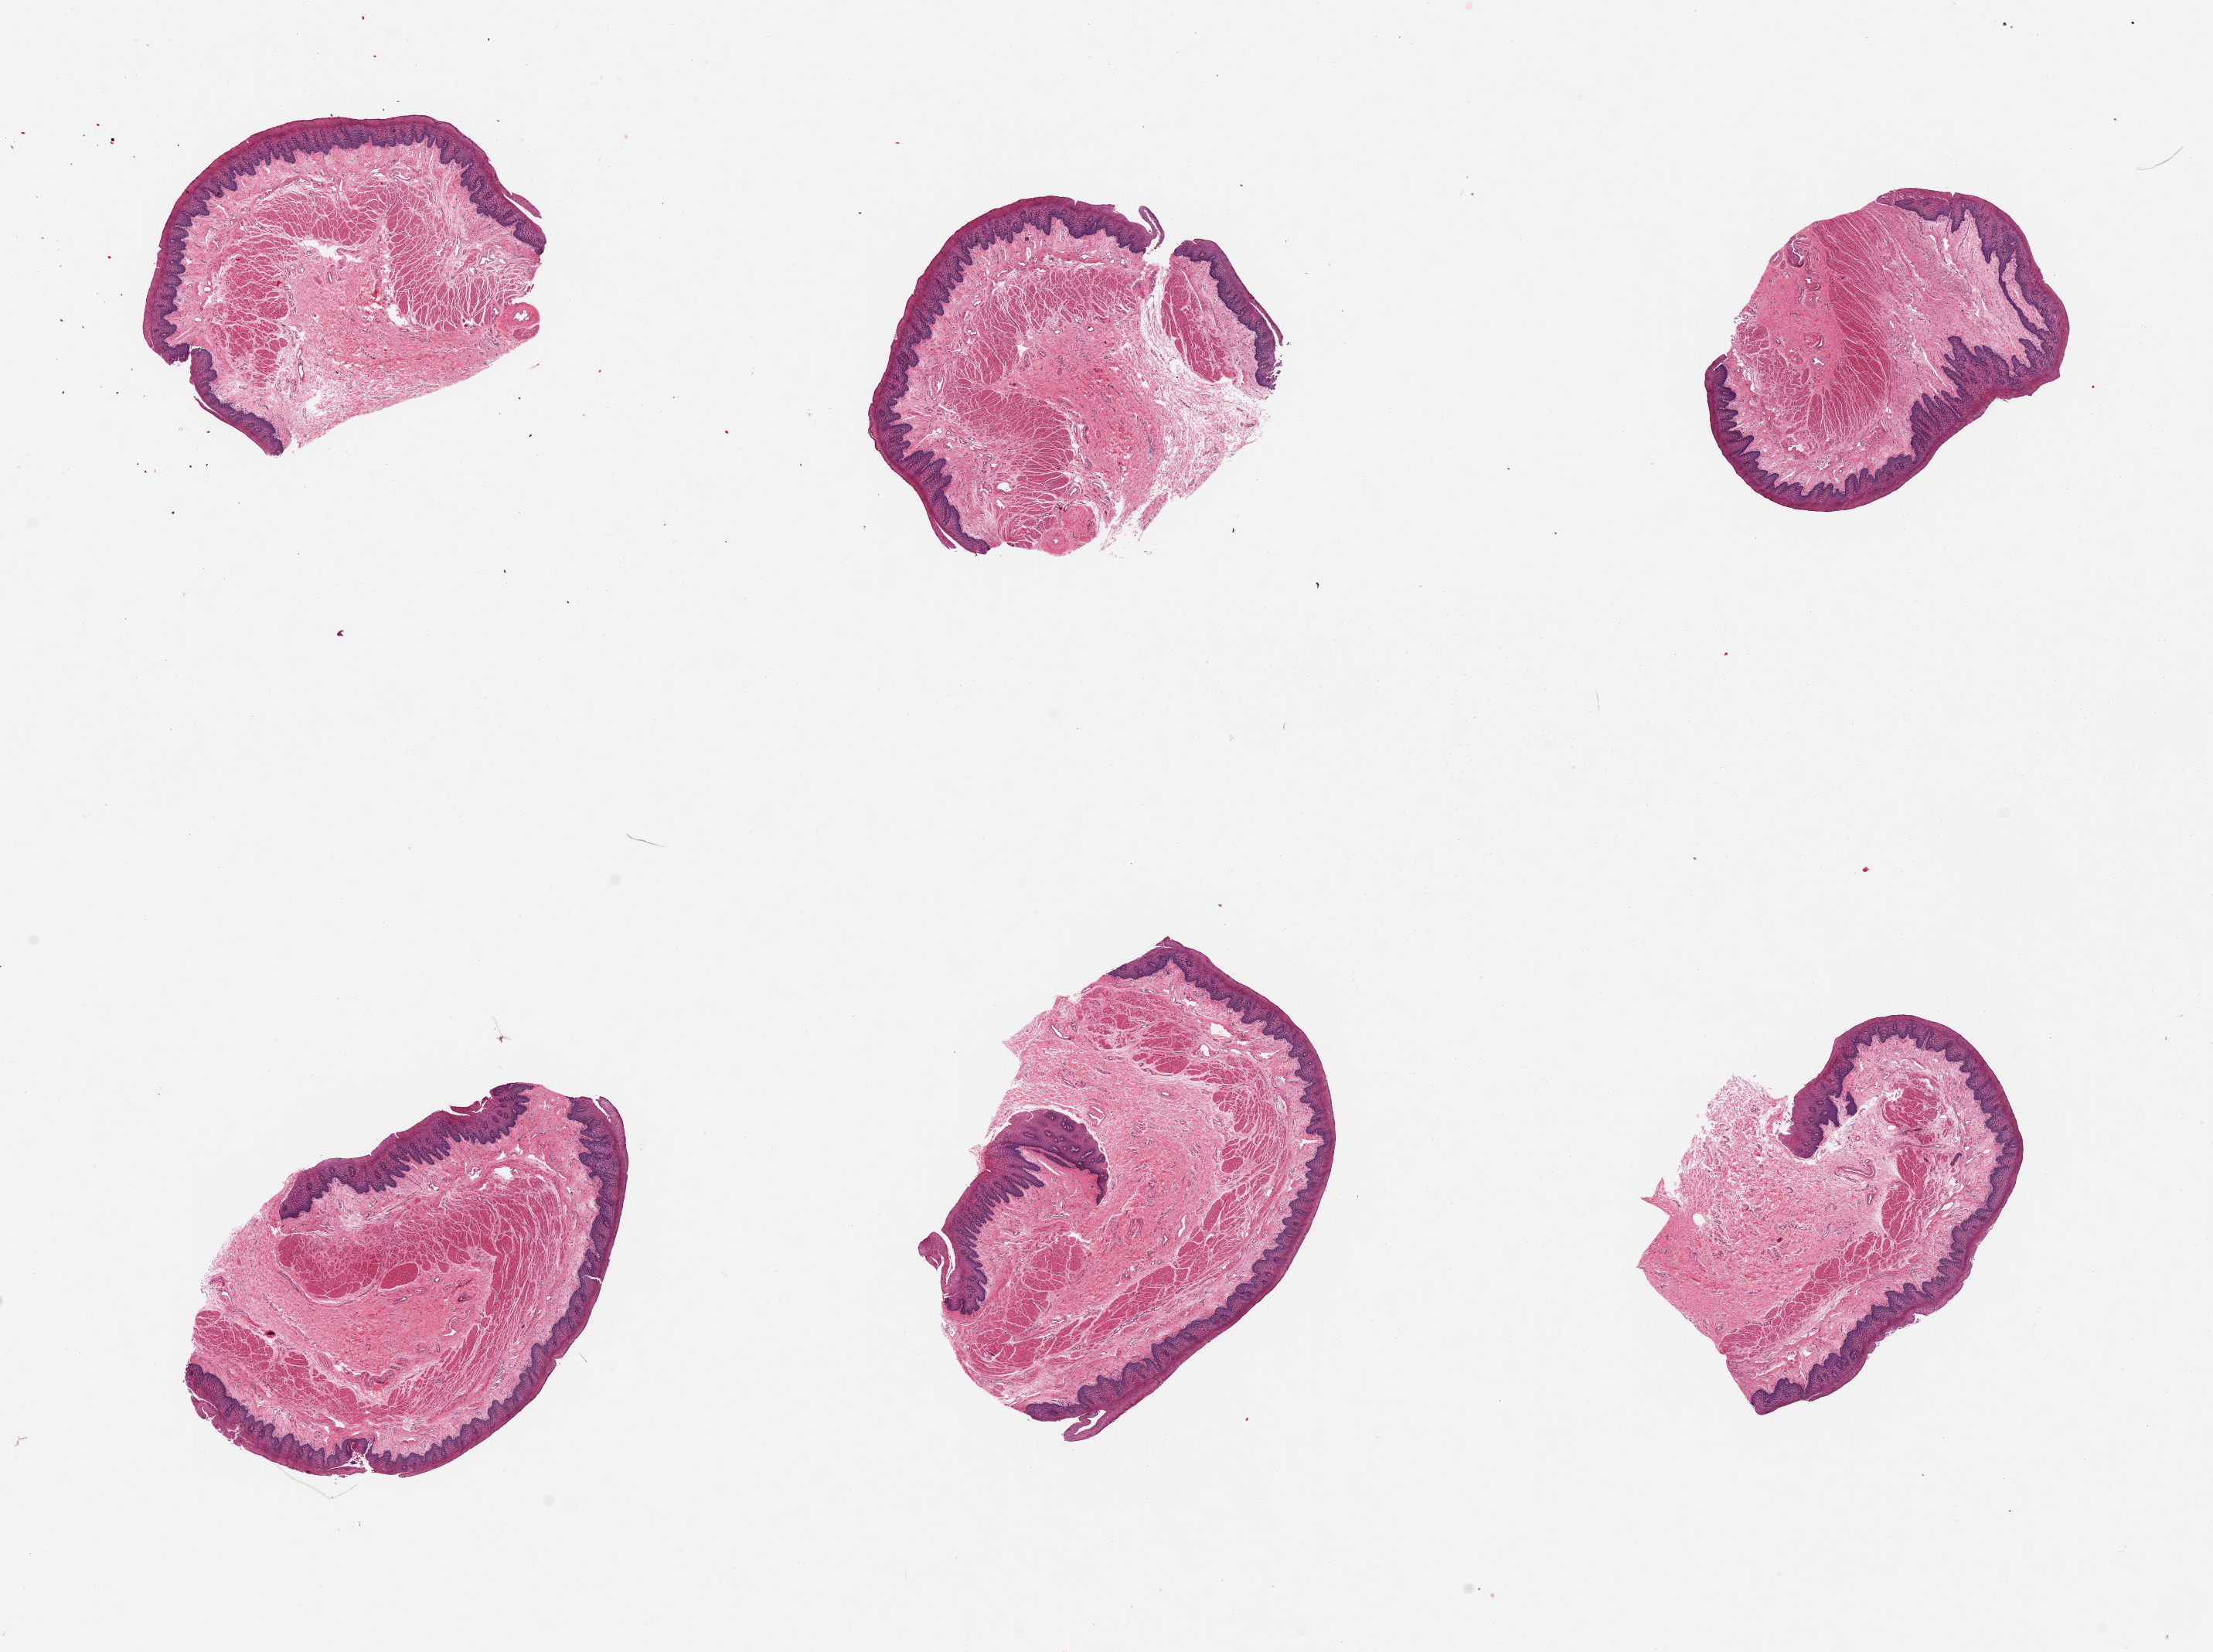
Digitized H&E-stained section, low-resolution overview of the scanned area, about 22.6 x 16.9 mm, PAXgene-fixed paraffin-embedded (PFPE) section, section of esophageal mucous membrane (target tissue), tissue donor sample. Donor sex: female.
• review note (as recorded): 6 pieces